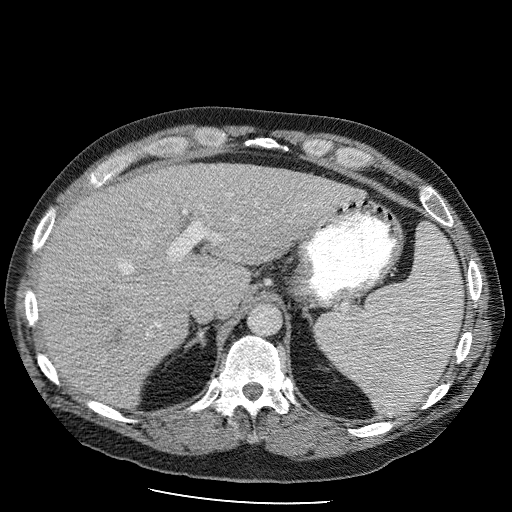
Contrast-enhanced abdominal CT (liver protocol), one axial slice; position 71 of 98 along the scan axis; 120 kVp; soft-tissue window (W 400 / L 40 HU); 2.5 mm slice thickness; 512 × 512 image matrix, field of view 400 × 400 mm. Case-level facts recorded for this patient, not image findings: diagnosis: hepatocellular carcinoma (patient treated with transarterial chemoembolisation; whether this scan precedes or follows treatment is not stated here); TNM stage (as recorded): Stage-II; Child-Pugh class: B; tumour nodularity: uninodular.
Outlined on this slice (semi-automatic segmentation, software-assisted and operator-edited):
- liver parenchyma outside the tumour (the mass and vessels are separate outlines, so this box may not span the whole liver): bounding box (x1, y1, x2, y2) in pixels: (36, 164, 363, 408)
- mass: (87, 301, 140, 354)
- liver vessels: (70, 220, 210, 370)